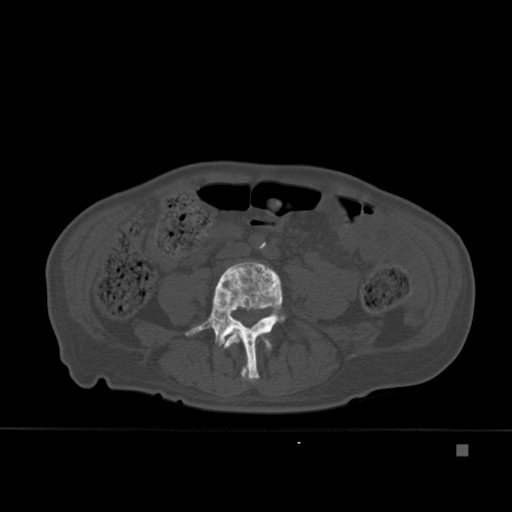
CT including the spine, one axial slice. Slice 124 of 451 in the series (ordered by position). Bone window (W 1800 / L 400 HU). 1.5 mm slice thickness. 512 × 512 image matrix, field of view 378 × 378 mm. Male patient, age 75 years. Case-level facts recorded for this patient, not image findings: primary cancer: prostate.
Structures marked on this image (semi-automatic segmentation, software-assisted and operator-edited):
- L3 vertebra: bounding box <224,333,272,380> (left, top, right, bottom; pixels)
- L4 vertebra: <185,262,285,382>